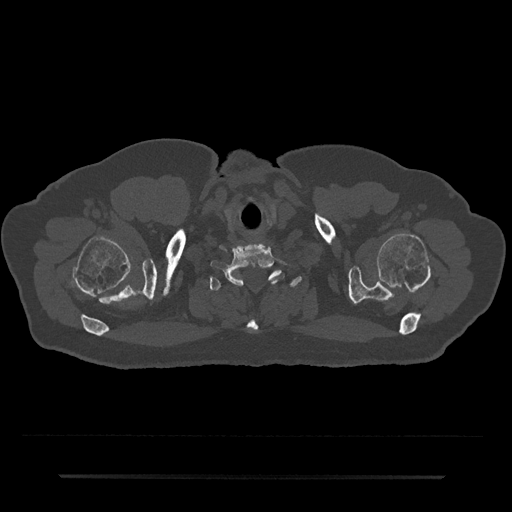
CT including the spine, one axial slice. Slice 661 of 797 in the series (ordered by position). Reconstruction kernel Br40s/3. 120 kVp. Bone window (W 1800 / L 400 HU). 0.5 mm slice thickness. 512 × 512 image matrix, field of view 437 × 437 mm. Male patient, age 69 years. From the clinical record (not read from this slice): primary cancer: prostate.
Structures marked on this image (semi-automatic segmentation, software-assisted and operator-edited):
- T1 vertebra: bounding box [x1, y1, x2, y2] px = [209, 270, 302, 333]